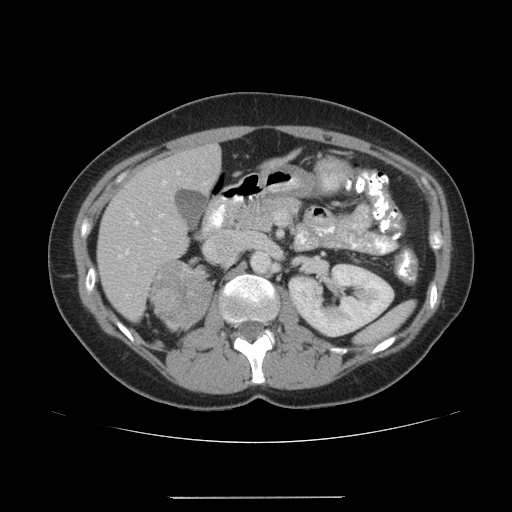
Contrast-enhanced abdominal CT, one axial slice. Slice 100 of 161 in the series (ordered by position). Intravenous contrast given. Soft-tissue window (W 400 / L 40 HU). 3.75 mm slice thickness. 512 × 512 image matrix. Female patient. From the clinical record (not read from this slice): diagnosis: adrenocortical carcinoma; tumour side: right adrenal.
Outlined on this slice (semi-automatic segmentation, software-assisted and operator-edited):
- mass: box from (x=152, y=261) to (x=214, y=331) px